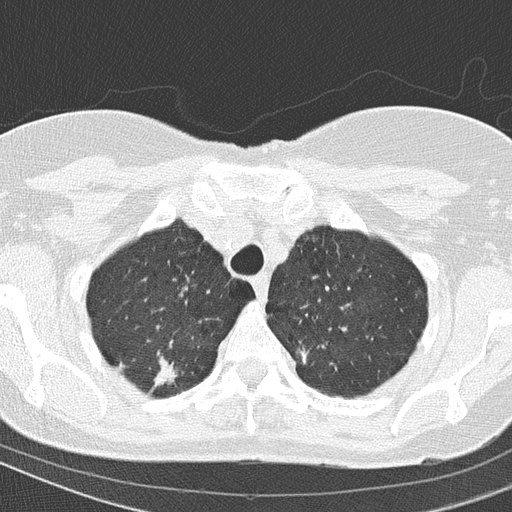
Low-dose screening chest CT, axial slice; baseline annual screen; lung window (W 1500 / L -600 HU); lung (sharp) reconstruction kernel (B50f); 512 × 512 image matrix, field of view 288 × 288 mm. Female participant, aged 67 years at enrolment.
- Expert reader's lesion annotation, bounding box (x1, y1, x2, y2) in pixels: (133, 347, 193, 398).
- Reader record for this screening exam (exam-level; its link to the box is not recorded): non-calcified nodule or mass ≥4 mm, right upper lobe, 15 × 14 mm, spiculated (stellate) margins, soft tissue attenuation.
- Later outcome: lung cancer diagnosed 63 days after this screen — adenocarcinoma, NOS, right upper lobe, moderately differentiated (G2), stage IA (AJCC 6th edition), 14 mm at pathology.